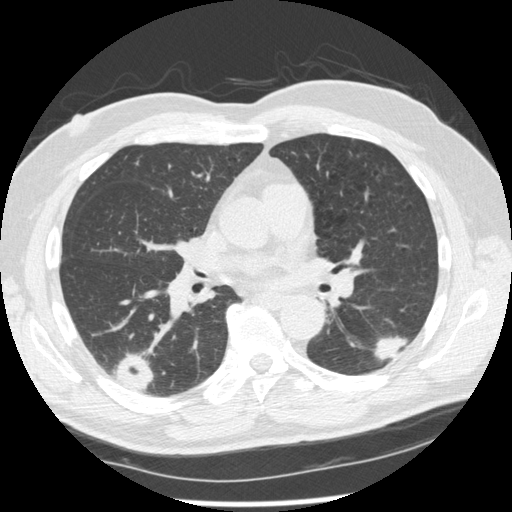
Low-dose screening chest CT, axial slice; second screening round (one year after baseline); lung window (W 1500 / L -600 HU); 1.25 mm slice thickness; standard (soft-tissue) reconstruction kernel (STANDARD); 120 kVp; slice 117 of 227 in the series. Male, age 74 years at enrolment.
Expert reader's lesion annotation, bounding box [x1, y1, x2, y2] px = [369, 314, 423, 368]. The screening reader recorded 7 non-calcified nodules or masses ≥4 mm on this exam (right upper lobe, right lower lobe, right upper lobe, right lower lobe, left lower lobe, left upper lobe, left upper lobe); which of them this box marks is not recorded. Official screen result: positive, other. Lung cancer was diagnosed 43 days after this screen: squamous cell carcinoma, NOS, left lower lobe, well differentiated (G1), stage IA (AJCC 6th edition), 28 mm at pathology.